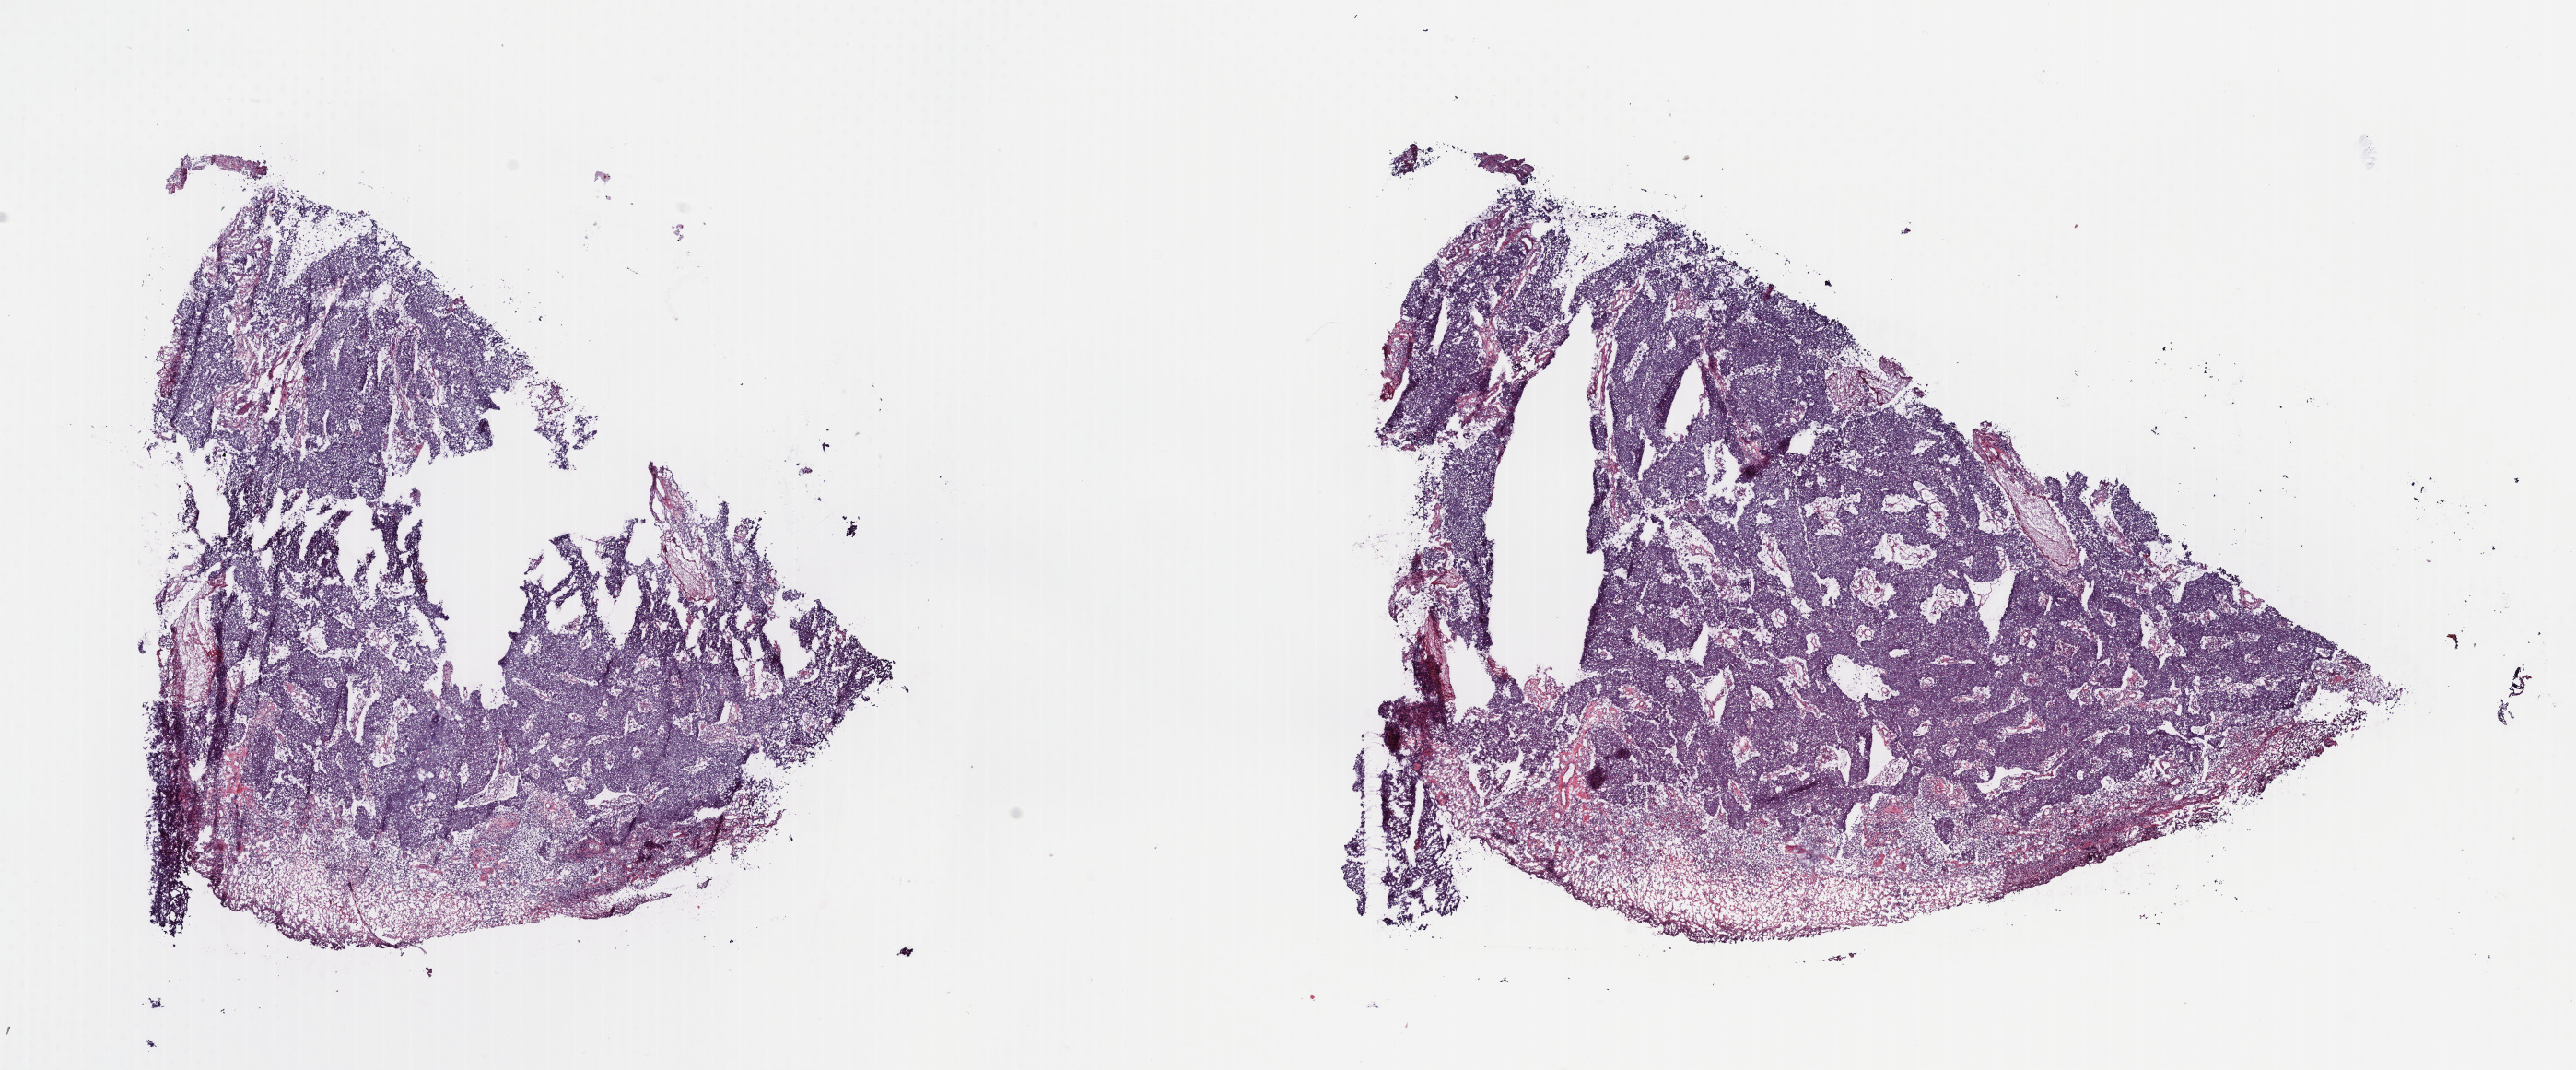
Digitized Hematoxylin and eosin (H&E) stained tissue section (whole slide) — a low-resolution overview of the entire scanned area, about 22.1 x 9.2 mm (acquisition: 40x scan); frozen section from the top of the tissue portion; primary tumour sample from the prostate. Patient: male, age at initial diagnosis 70 years. Gleason score: 8 (5+3). Composition of this section per pathologist review: tumour cells 90%, tumour nuclei 90%, normal cells 0%, stromal cells 7%, necrosis 3%. Inflammatory infiltration, as recorded: lymphocyte infiltration 0%, monocyte infiltration 0%, neutrophil infiltration 0%.
Diagnosis: Adenocarcinoma, NOS (prostate gland). Laterality: bilateral.